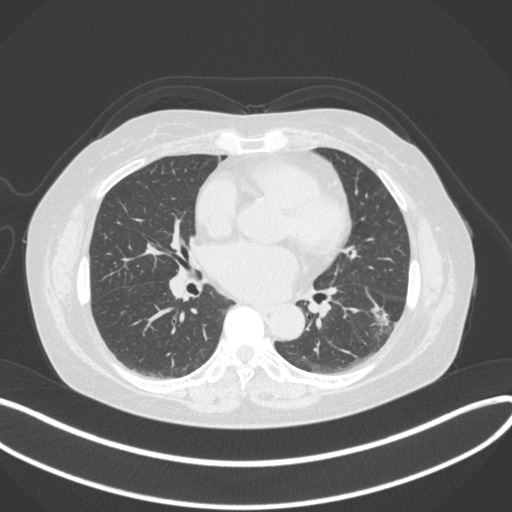
Chest CT, one axial slice. Slice 171 of 373 in the series (ordered by position). 120 kVp. Lung window (W 1500 / L -600 HU). 1 mm slice thickness. 512 × 512 image matrix. Female patient, age 67 years. Case-level facts recorded for this patient, not image findings: clinical TNM (as recorded): T1c N0 M0; histopathological grade: G2.
Annotated regions visible in this slice (rectangle marked by the reading radiologist):
- lung tumour (recorded histology: adenocarcinoma): bounding box <365,300,395,332> (left, top, right, bottom; pixels)